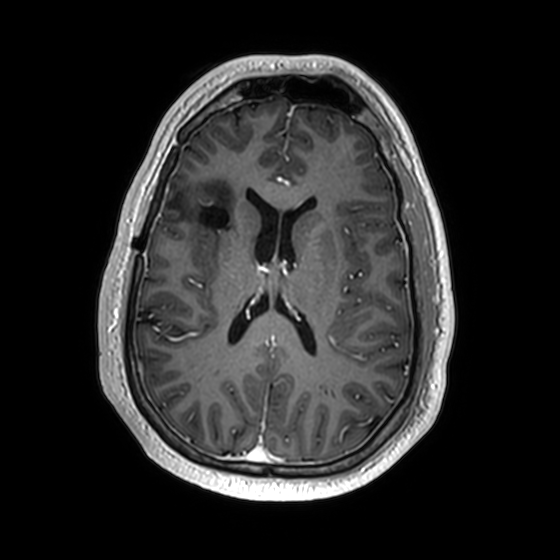
Brain MRI from a brain-tumour surgery series, one axial slice; position 76 of 174 along the scan axis; T1-weighted post-contrast; 560 × 560 image matrix. From the clinical record (not read from this slice): histopathology: Astrocytoma; WHO grade: 2; IDH mutation: yes; tumour location: Right Insular.
Structures marked on this image (outlined manually by an expert reader):
- previous resection cavity: bounding box [x1, y1, x2, y2] px = [200, 206, 229, 230]